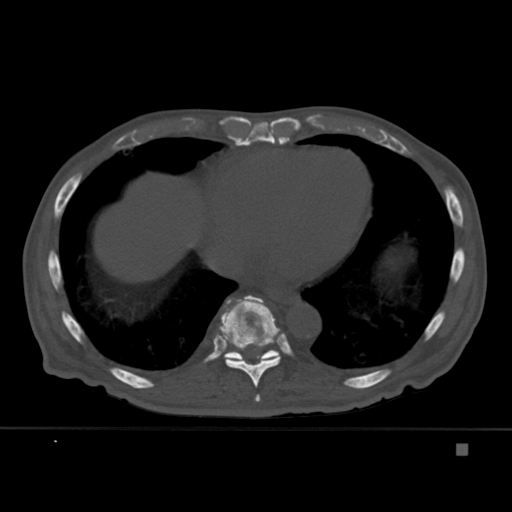
CT including the spine, one axial slice. Position 243 of 451 along the scan axis. Bone window (W 1800 / L 400 HU). 1.5 mm slice thickness. 512 × 512 image matrix. Patient: male, 75 years. Case-level facts recorded for this patient, not image findings: primary cancer: prostate.
Outlined on this slice (semi-automatic segmentation, software-assisted and operator-edited):
- T10 vertebra: bounding box [x1, y1, x2, y2] px = [224, 300, 281, 361]
- T8 vertebra: [254, 394, 260, 402]
- T9 vertebra: [213, 295, 289, 402]